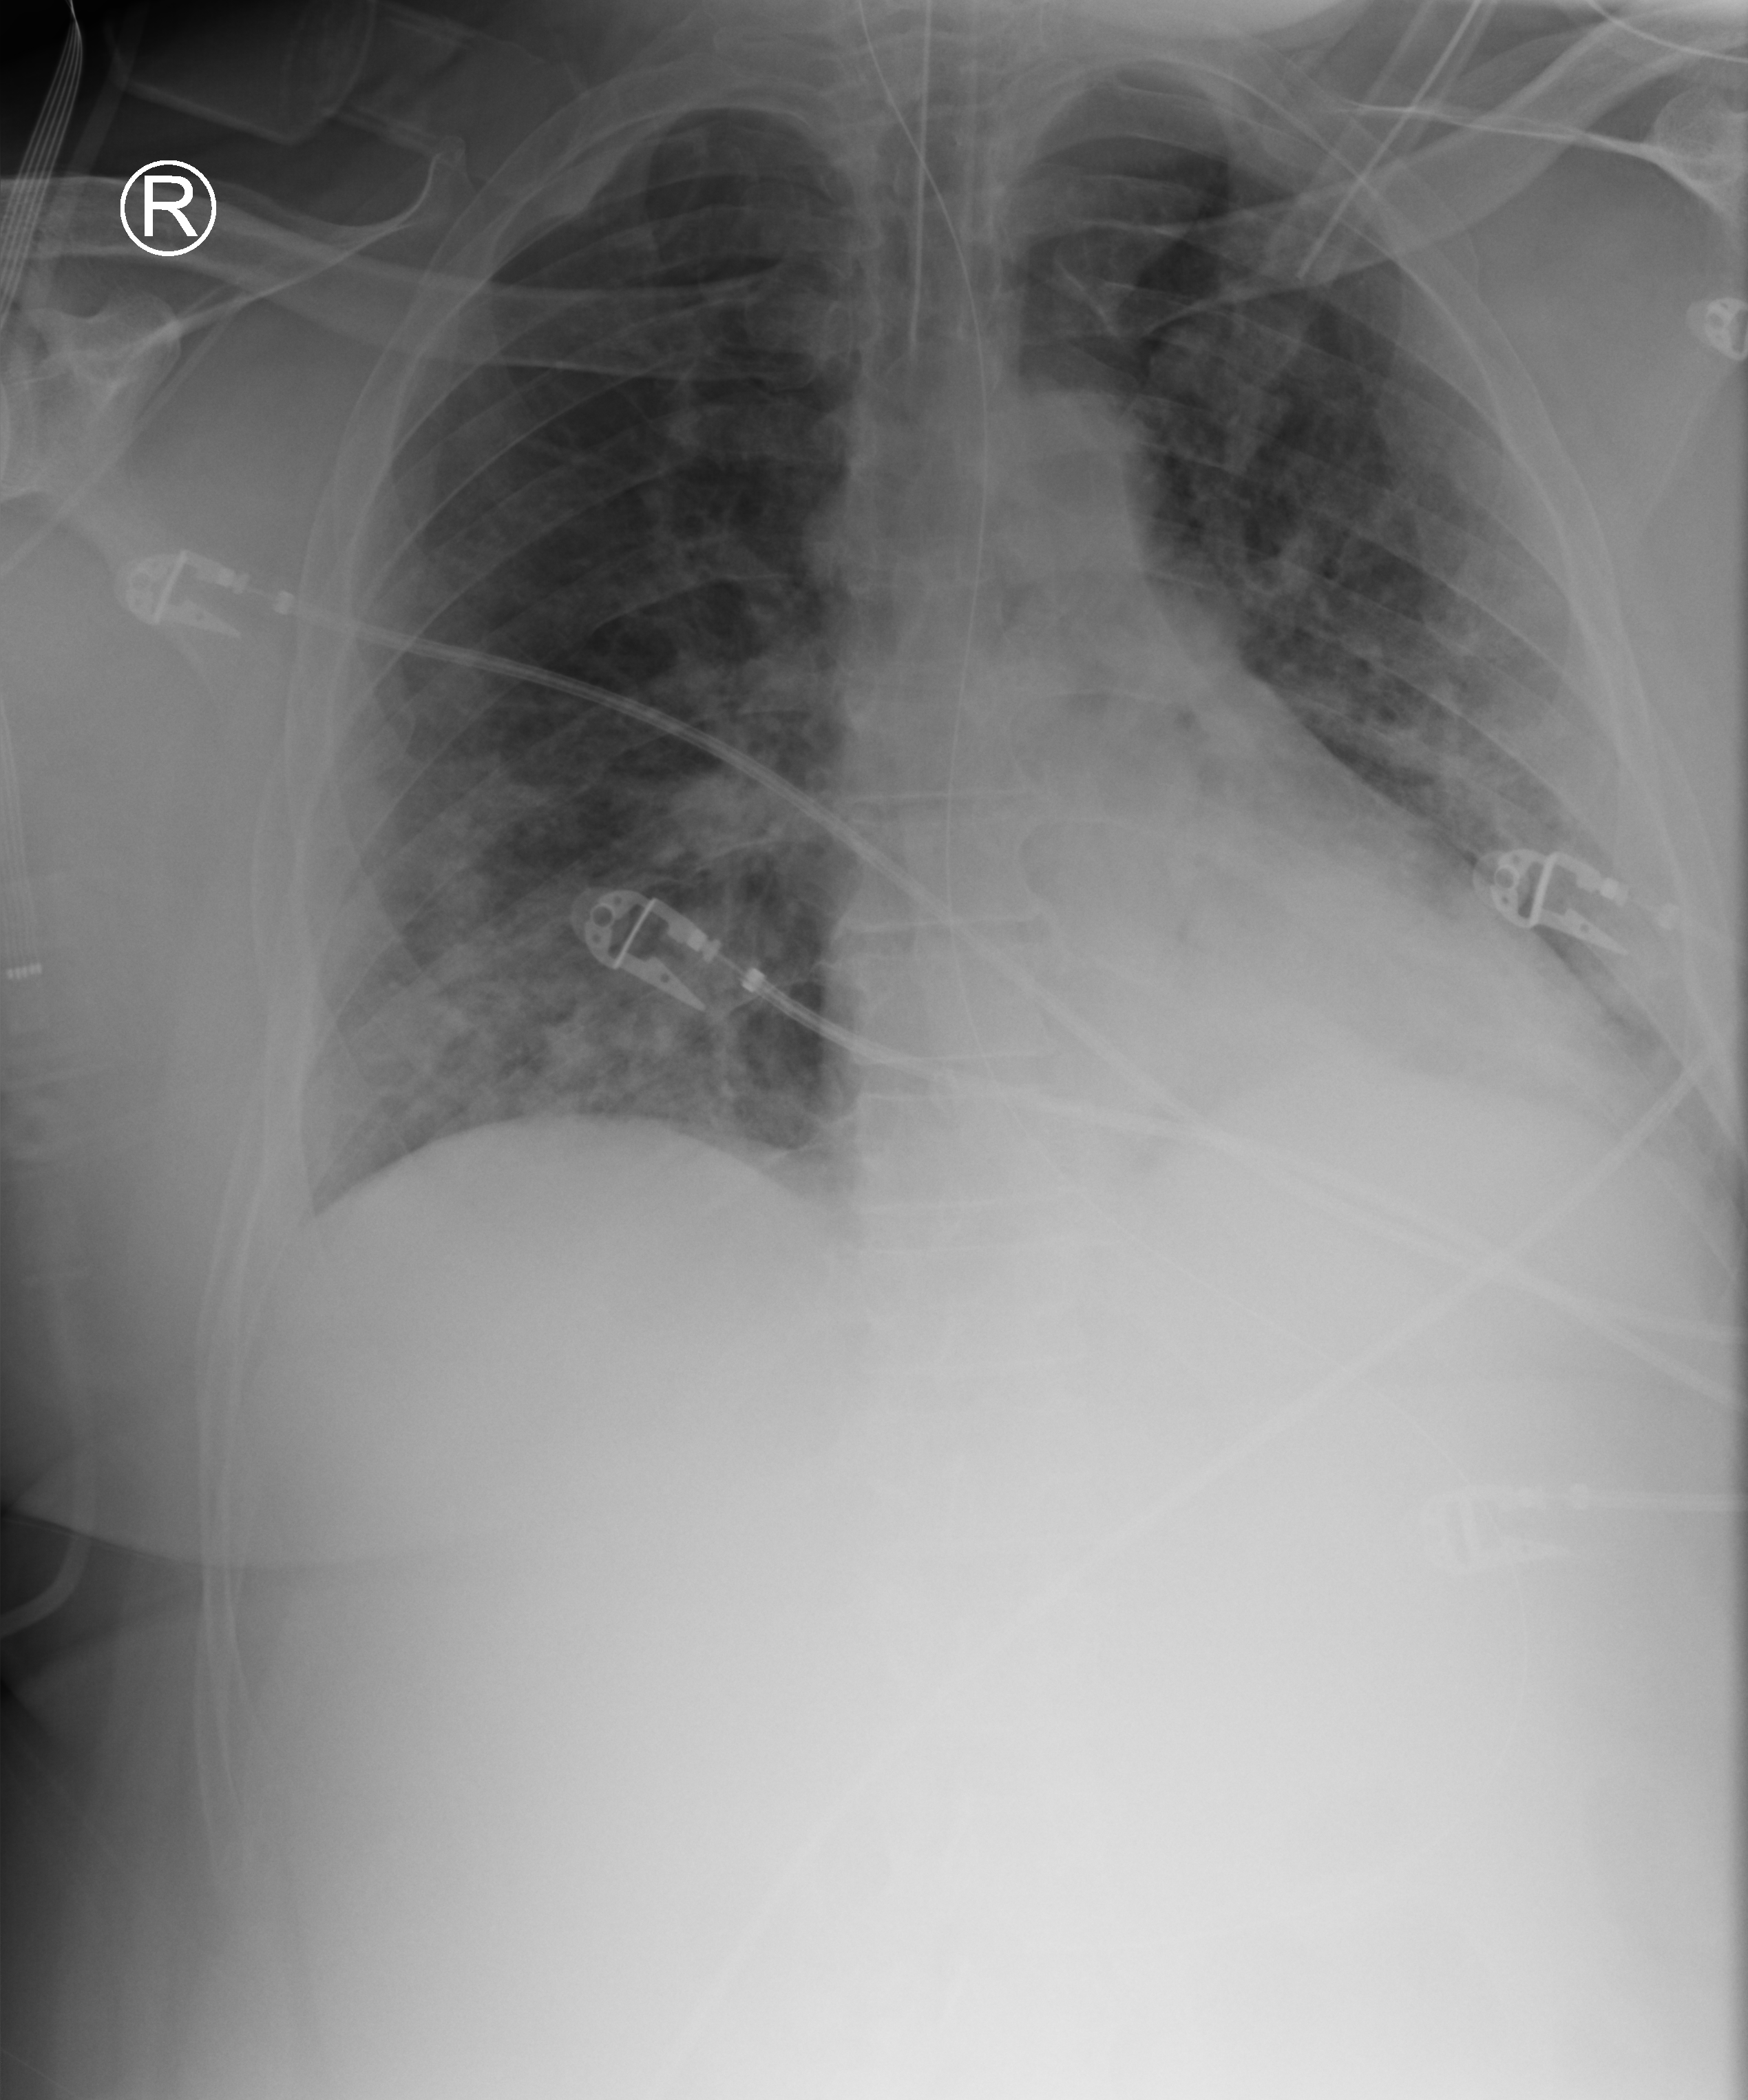
Portable chest radiograph, anteroposterior (AP) projection. Patient hospitalised with COVID-19; male, aged 18–59 years.
From the hospital-stay record, not from the radiograph (when in the stay this image was taken is not recorded): admitted to intensive care during this hospital stay: yes; mechanically ventilated during this hospital stay: yes; length of hospital stay: 15 days.